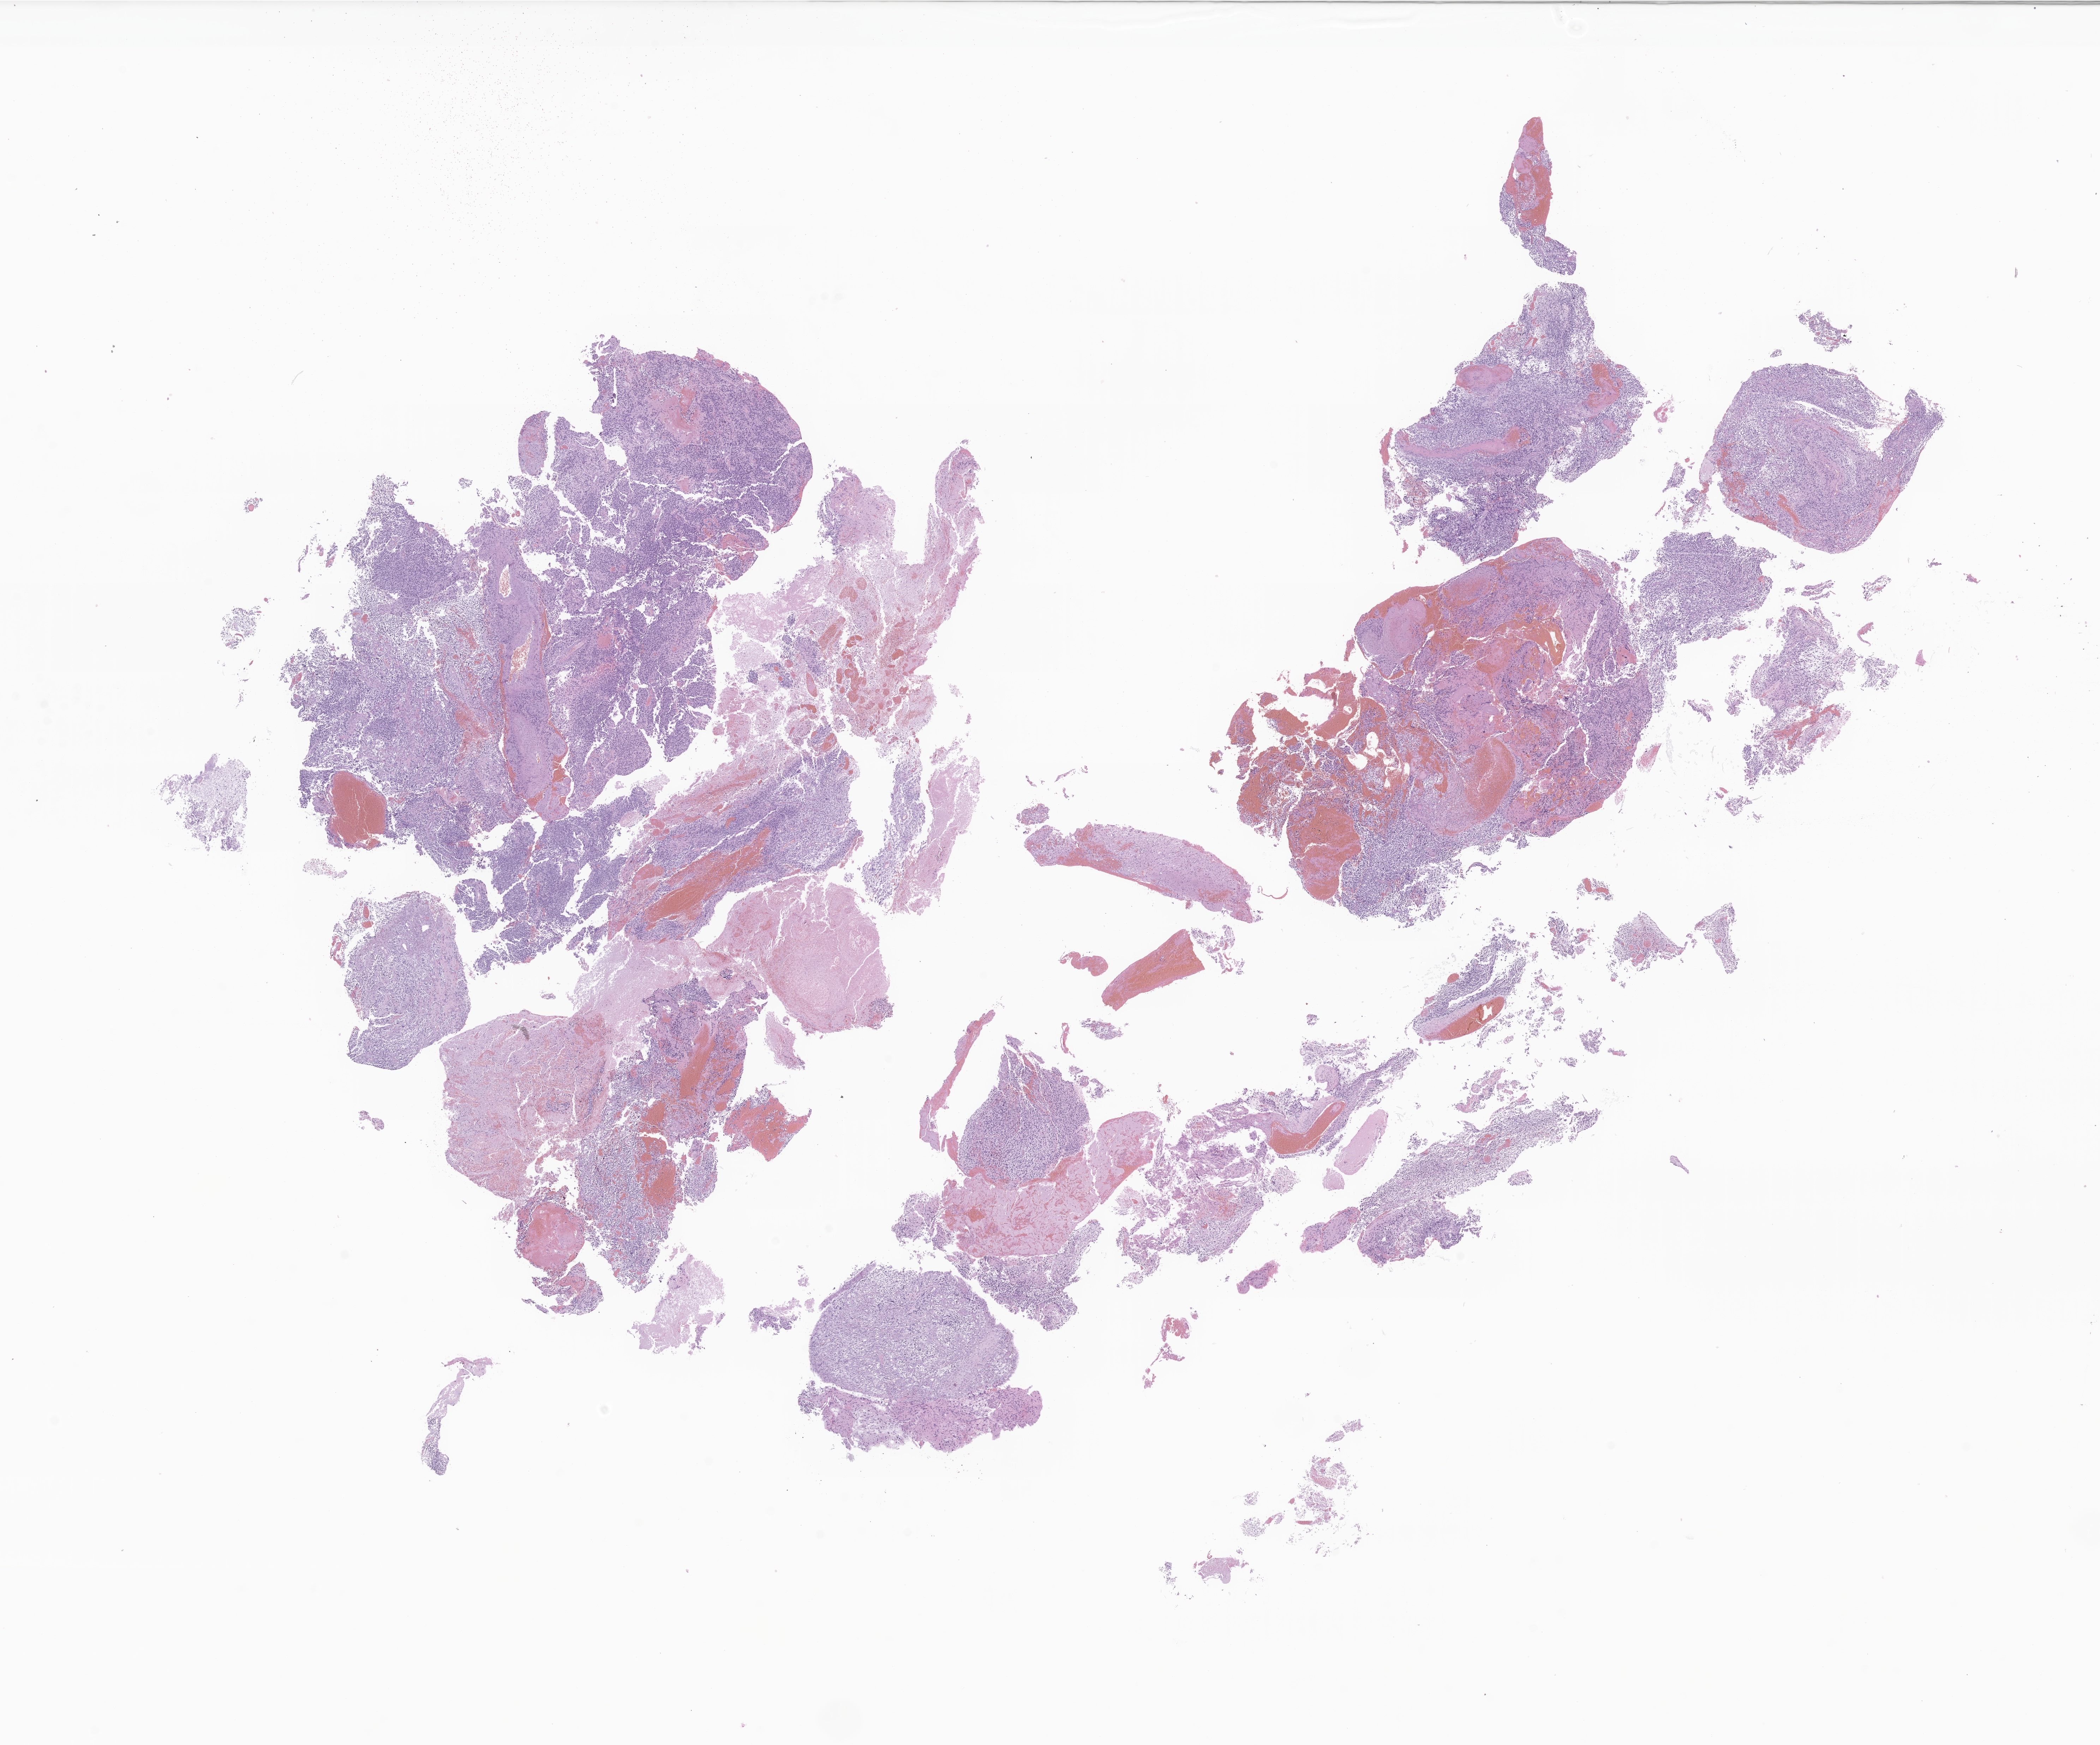
Hematoxylin and eosin (H&E) whole-slide image of tumor tissue from the brain — shown as a low-resolution overview of the whole scanned area (about 25.1 x 20.8 mm), FFPE section. Male patient, age 113 months (9 years 5 months).
* diagnosis (ICD-O-3 morphology term): Glioma, malignant